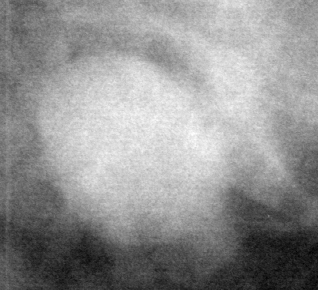
Crop from a digitized film mammogram around one marked abnormality; left breast; MLO view; BI-RADS breast density category 3 (scale 1–4).
- Finding: mass, shape oval, margins circumscribed; BI-RADS assessment category 3; subtlety rating 5 on a 1 (subtle) to 5 (obvious) scale; pathology (as recorded): benign.